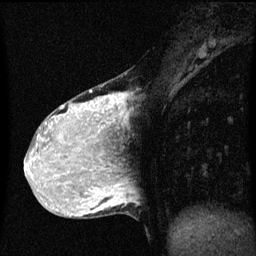
Breast MRI (dynamic contrast-enhanced), one sagittal slice. Position 22 of 60 along the scan axis. Dynamic contrast-enhanced series, image 2 of 3 at this slice position (ordered by acquisition). 1.5 T. TE 4.2 ms, TR 8 ms. 2 mm slice thickness. 256 × 256 image matrix, field of view 200 × 200 mm. Patient: female, 36 years.
Annotated regions visible in this slice (semi-automatic segmentation, software-assisted and operator-edited):
- analysis volume of interest (the breast-tissue region the enhancement analysis was run in; not a lesion): box from (x=33, y=74) to (x=126, y=169) px
- tumour enhancement mask (voxels above the 70 % enhancement threshold inside the analysis volume of interest): (x=35, y=90)–(x=121, y=169)